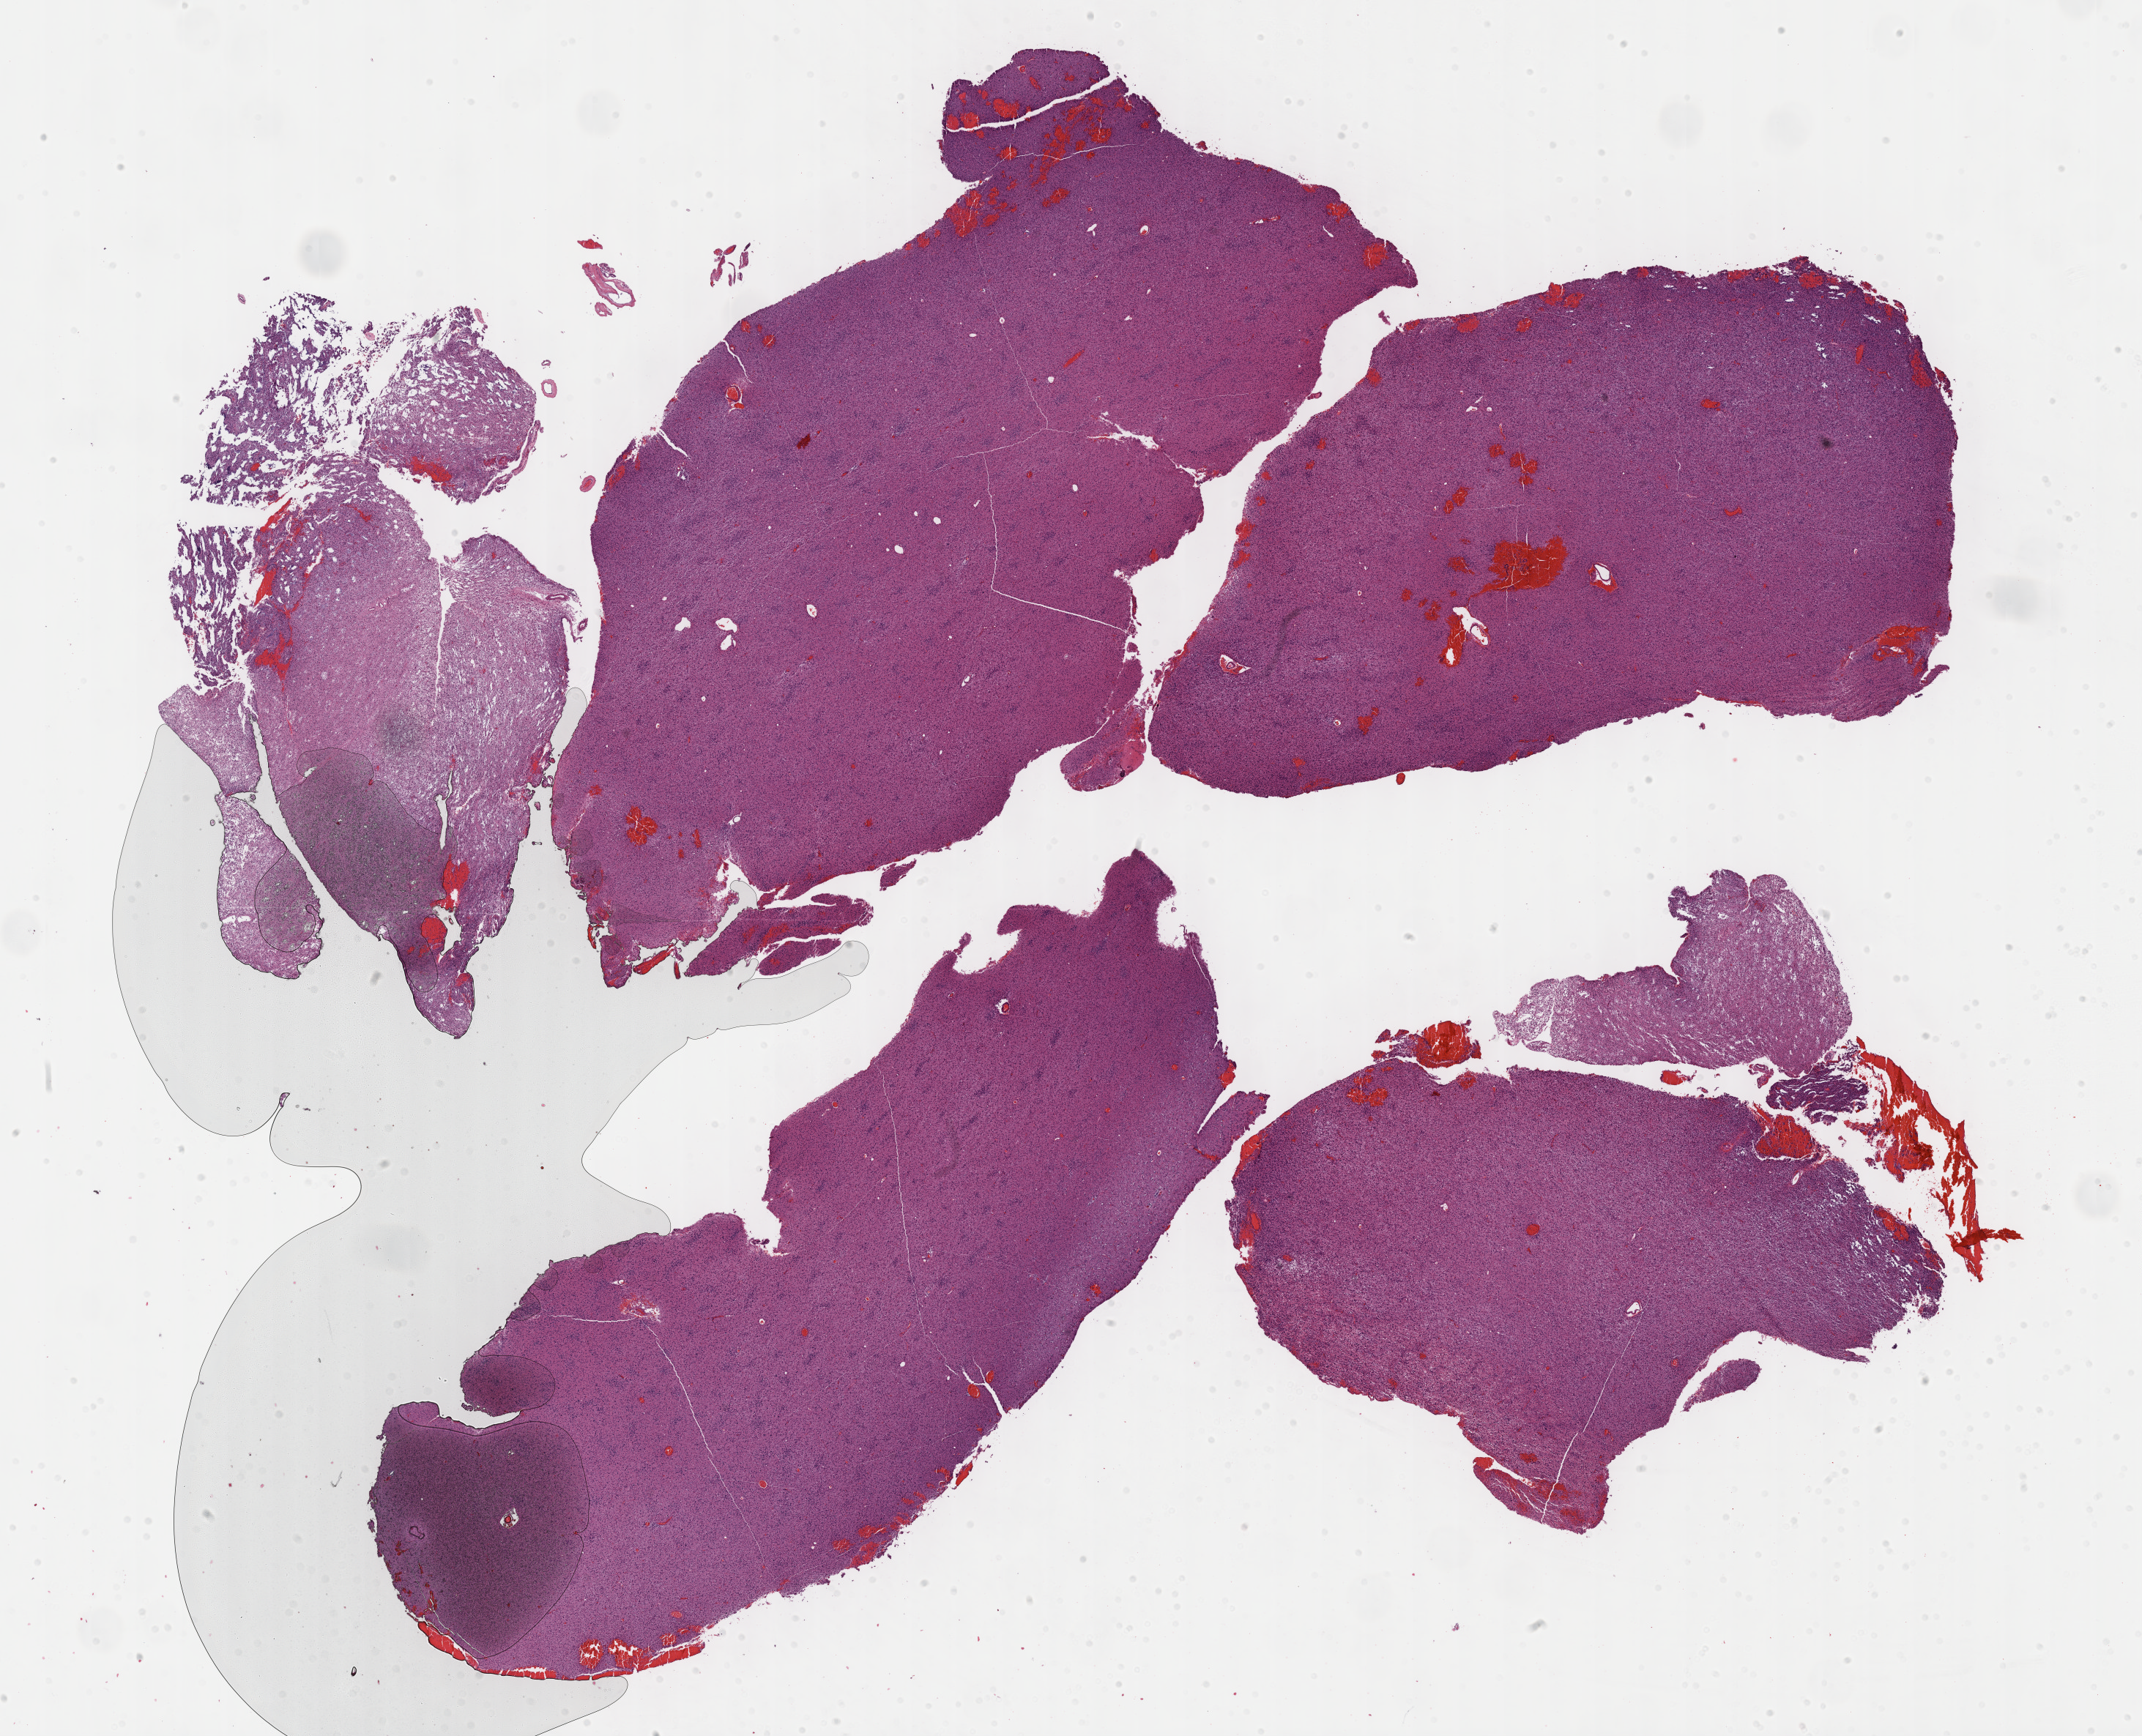
H&E-stained whole-slide image, a low-resolution overview of the entire scanned area, about 23.7 x 19.2 mm (acquisition: 40x scan); formalin-fixed paraffin-embedded (FFPE) diagnostic section; brain, primary tumour sample. Patient: male, age at initial diagnosis 28 years. Histologic grade: G2 (moderately differentiated).
Pathologic diagnosis: Mixed glioma. Laterality: right.